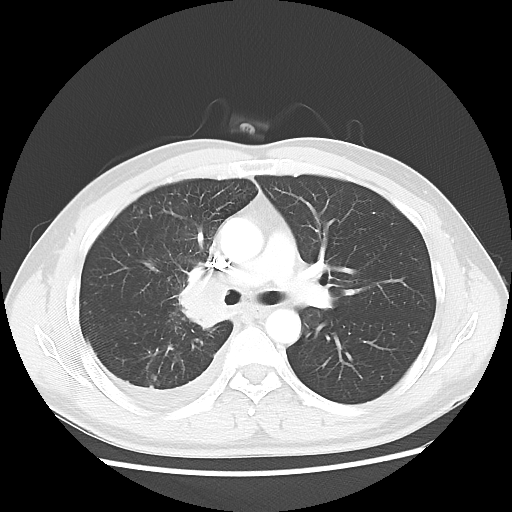
Chest CT, one axial slice; reconstruction kernel LUNG; lung window (W 1500 / L -600 HU); 5 mm slice thickness; 512 × 512 image matrix, field of view 360 × 360 mm. Male patient, age 46 years. Case-level facts recorded for this patient, not image findings: clinical TNM (as recorded): T2 N3 M1.
Outlined on this slice (rectangle marked by the reading radiologist):
- lung tumour (recorded histology: adenocarcinoma): bounding box [x1, y1, x2, y2] px = [172, 270, 228, 336]